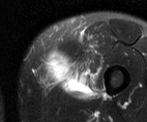
MRI of an extremity soft-tissue mass, one axial slice; position 12 of 52 along the scan axis; T2-weighted fat-saturated; MR volume resampled by the dataset authors to the PET/CT grid (not the native acquisition matrix); 3.27 mm slice thickness; 147 × 122 image matrix, field of view 144 × 119 mm. Male patient. Case-level facts recorded for this patient, not image findings: histological type: pleiomorphic liposarcoma; grade: high; site of the primary tumour: left thigh.
Annotated regions visible in this slice (expert contour drawn on MRI and transferred to this co-registered scan by the dataset authors):
- gross tumour volume including surrounding oedema: bounding box <39,43,101,97> (left, top, right, bottom; pixels)
- gross tumour volume (mass): <39,43,74,86>